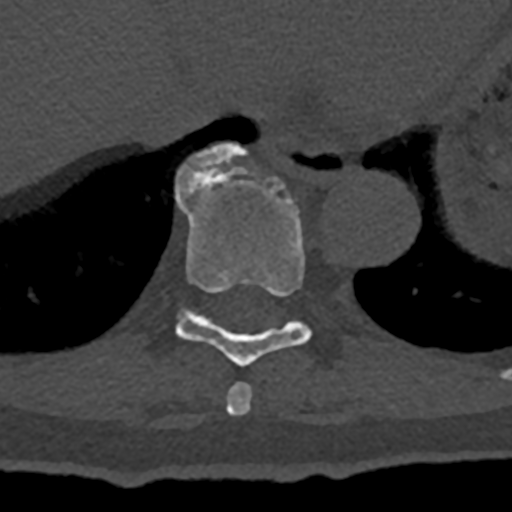
CT including the spine, one axial slice. Slice 649 of 797 in the series (ordered by position). 120 kVp. Bone window (W 1800 / L 400 HU). 0.5 mm slice thickness. 512 × 512 image matrix, field of view 160 × 160 mm. Male patient, age 74 years. Case-level facts recorded for this patient, not image findings: primary cancer: renal.
Outlined on this slice (semi-automatic segmentation, software-assisted and operator-edited):
- T10 vertebra: box from (x=175, y=144) to (x=248, y=201) px
- T8 vertebra: (x=226, y=382)–(x=252, y=415)
- T9 vertebra: (x=175, y=167)–(x=312, y=367)